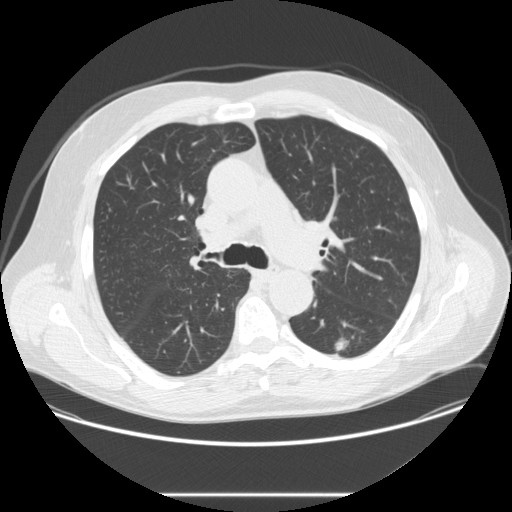
Low-dose screening chest CT, one axial slice. Reconstruction kernel STANDARD. 120 kVp. Lung window (W 1500 / L -600 HU). 512 × 512 image matrix.
Annotated regions visible in this slice (expert manual segmentation):
- lesion 1 (tumor, lower lobe of left lung): box from (x=335, y=339) to (x=348, y=351) px